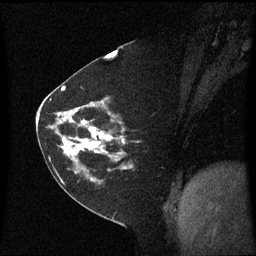
Breast MRI (dynamic contrast-enhanced), one sagittal slice; dynamic contrast-enhanced series, image 2 of 3 at this slice position (ordered by acquisition); 1.5 T; TE 4.2 ms, TR 8.4 ms; 2 mm slice thickness; 256 × 256 image matrix, field of view 210 × 210 mm. Patient: female, 60 years. From the clinical record (not read from this slice): setting: breast cancer imaged before/during neoadjuvant chemotherapy; receptor status: triple-negative.
Outlined on this slice (semi-automatically segmented with operator editing):
- analysis volume of interest (the breast-tissue region the enhancement analysis was run in; not a lesion): bounding box (x1, y1, x2, y2) in pixels: (45, 99, 135, 182)
- tumour enhancement mask (voxels above the 70 % enhancement threshold inside the analysis volume of interest): (59, 113, 125, 168)